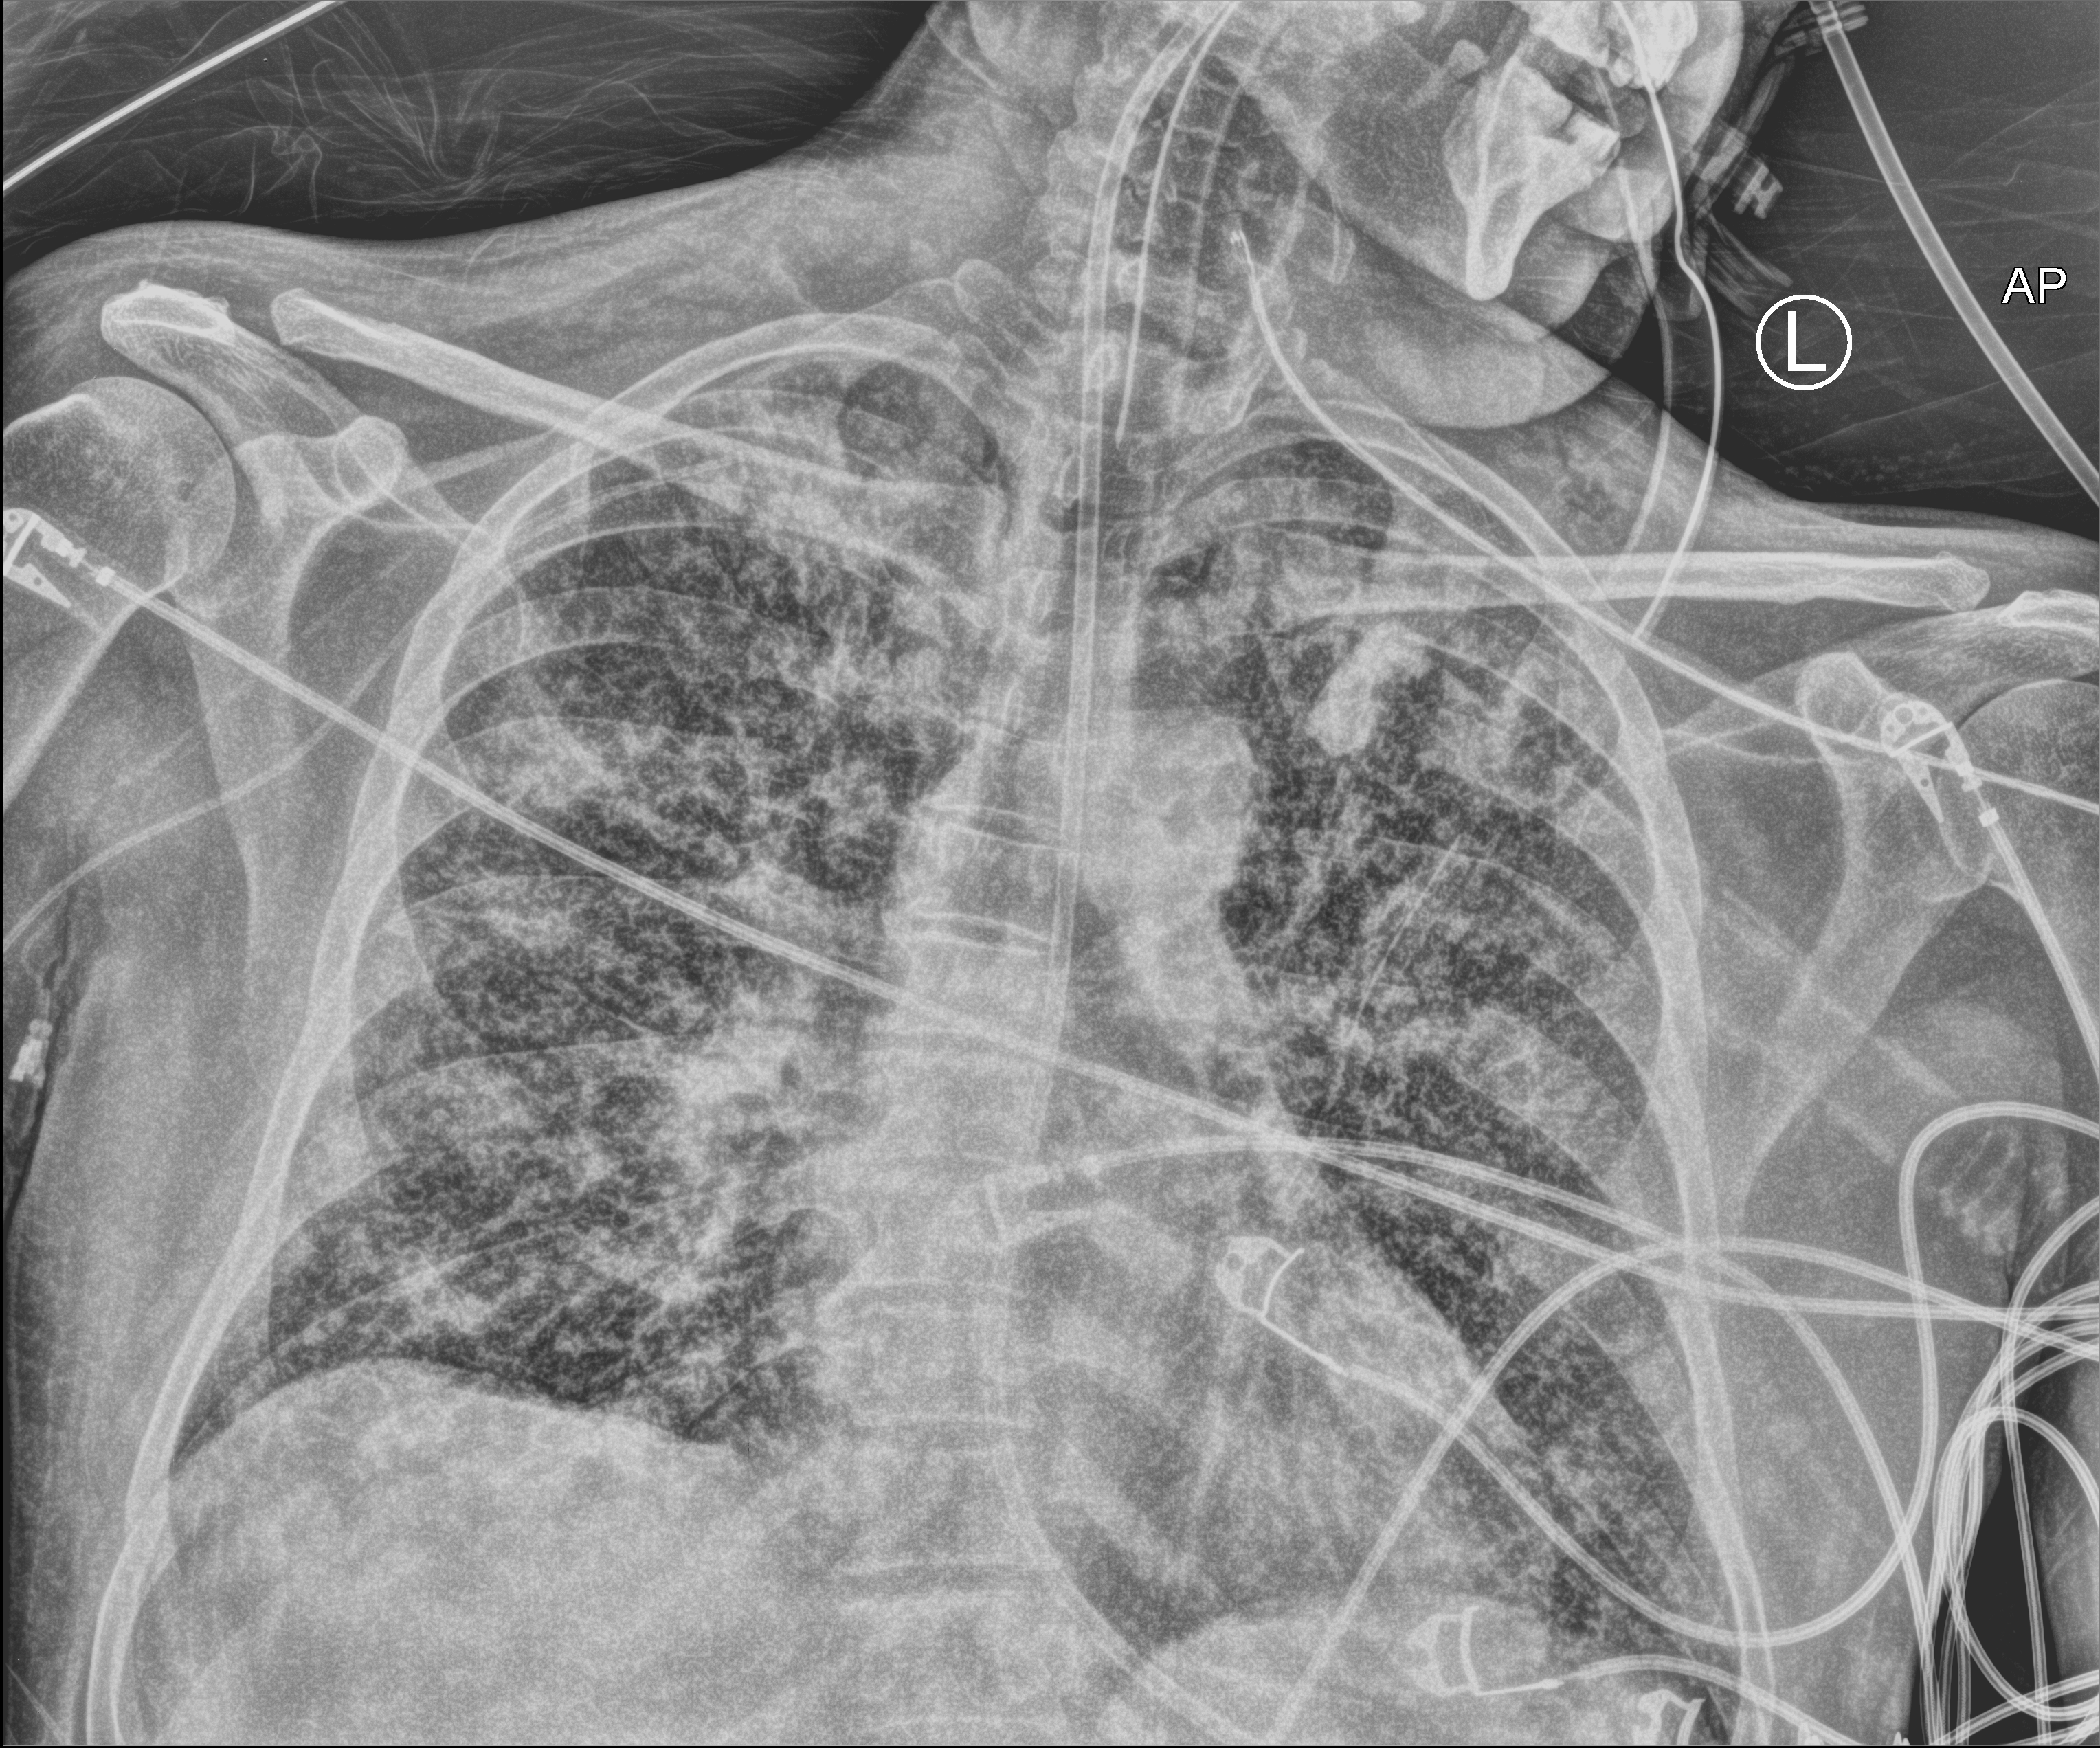
Chest X-ray (portable); anteroposterior (AP) projection. Male patient hospitalised with COVID-19, age 18–59 years.
Admission-level facts for this patient (not findings on this image; timing relative to this image not recorded): admitted to intensive care during this hospital stay: yes; other chronic lung disease (admission record): no.